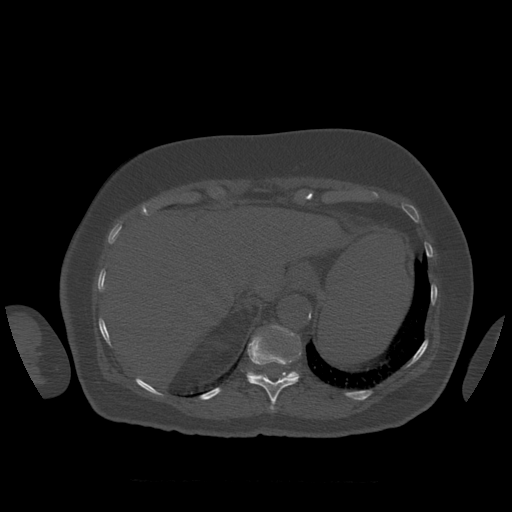
CT including the spine, one axial slice; reconstruction kernel STANDARD; 120 kVp; bone window (W 1800 / L 400 HU); 1.25 mm slice thickness; 512 × 512 image matrix, field of view 404 × 404 mm. Patient age 81 years. Case-level facts recorded for this patient, not image findings: primary cancer: renal; vertebrae with lytic lesions (as recorded): L1.
Structures marked on this image (semi-automatic segmentation, software-assisted and operator-edited):
- T11 vertebra: bounding box <247,328,301,412> (left, top, right, bottom; pixels)
- T12 vertebra: <247,326,300,379>